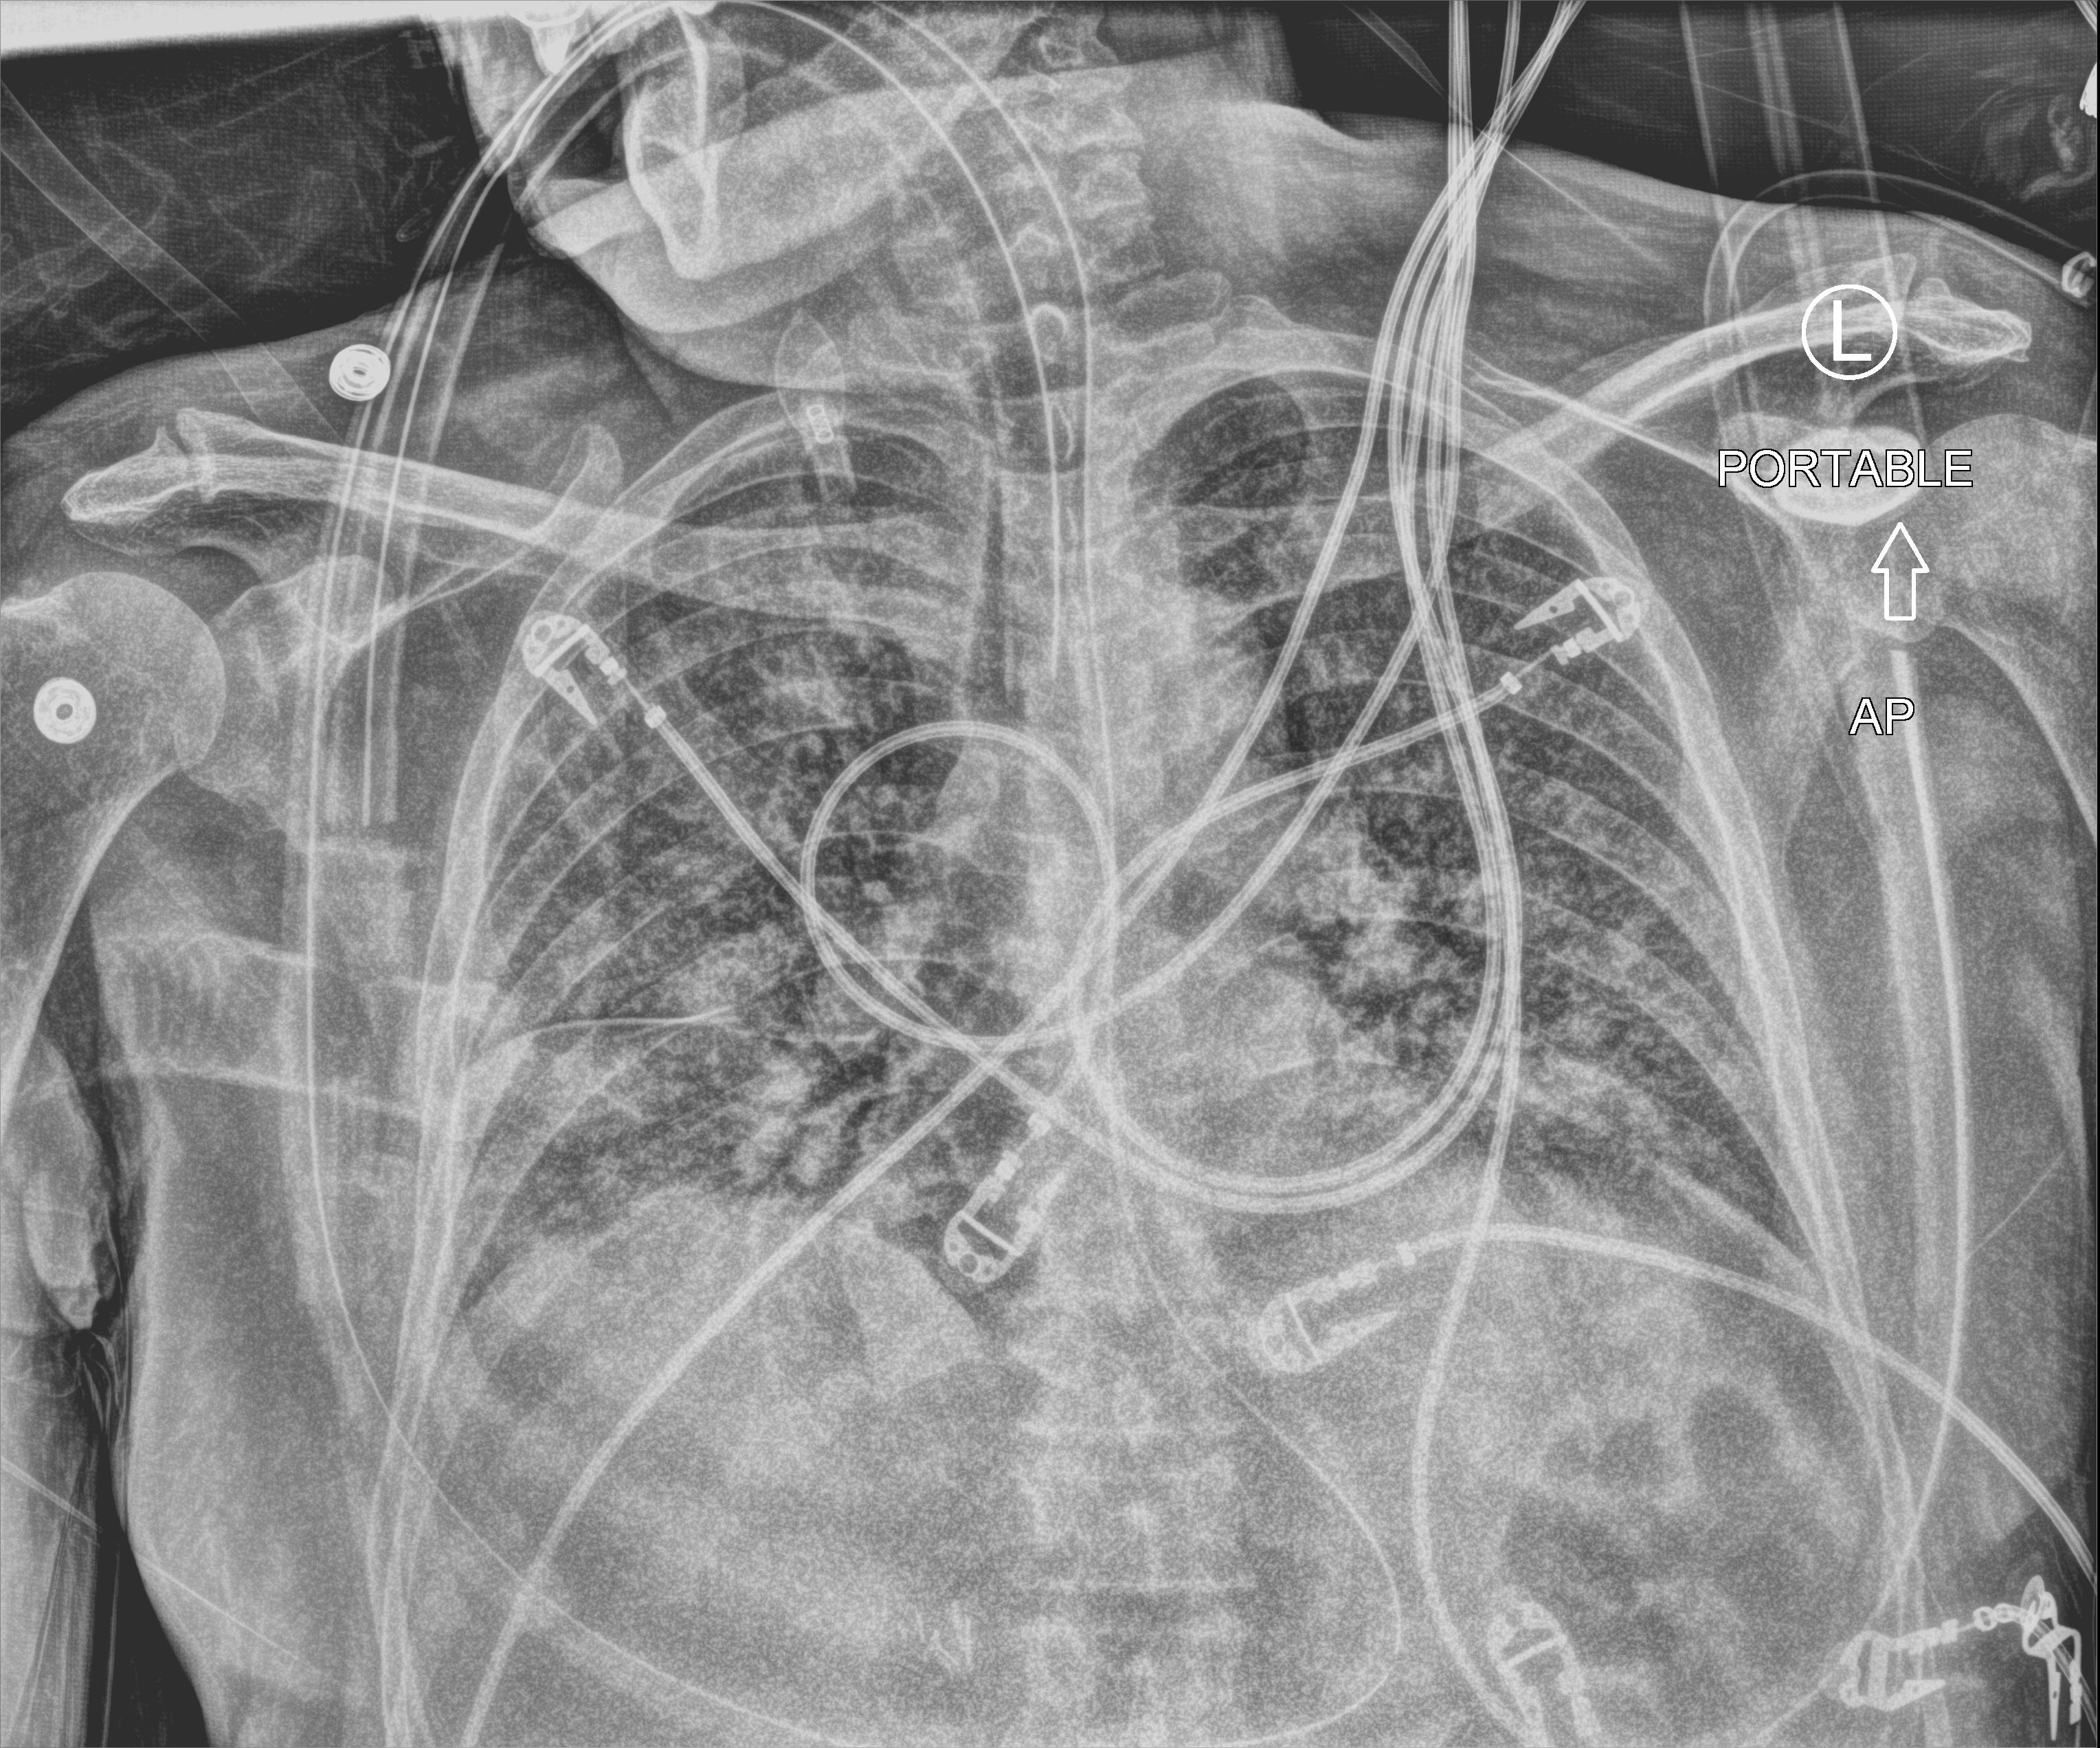
Chest X-ray (portable), anteroposterior (AP) projection. Patient hospitalised with COVID-19; male, aged 60–74 years.
Admission-level facts for this patient (not findings on this image; timing relative to this image not recorded):
- mechanically ventilated during this hospital stay: yes
- smoking status (admission record): never
- length of hospital stay: 23 days